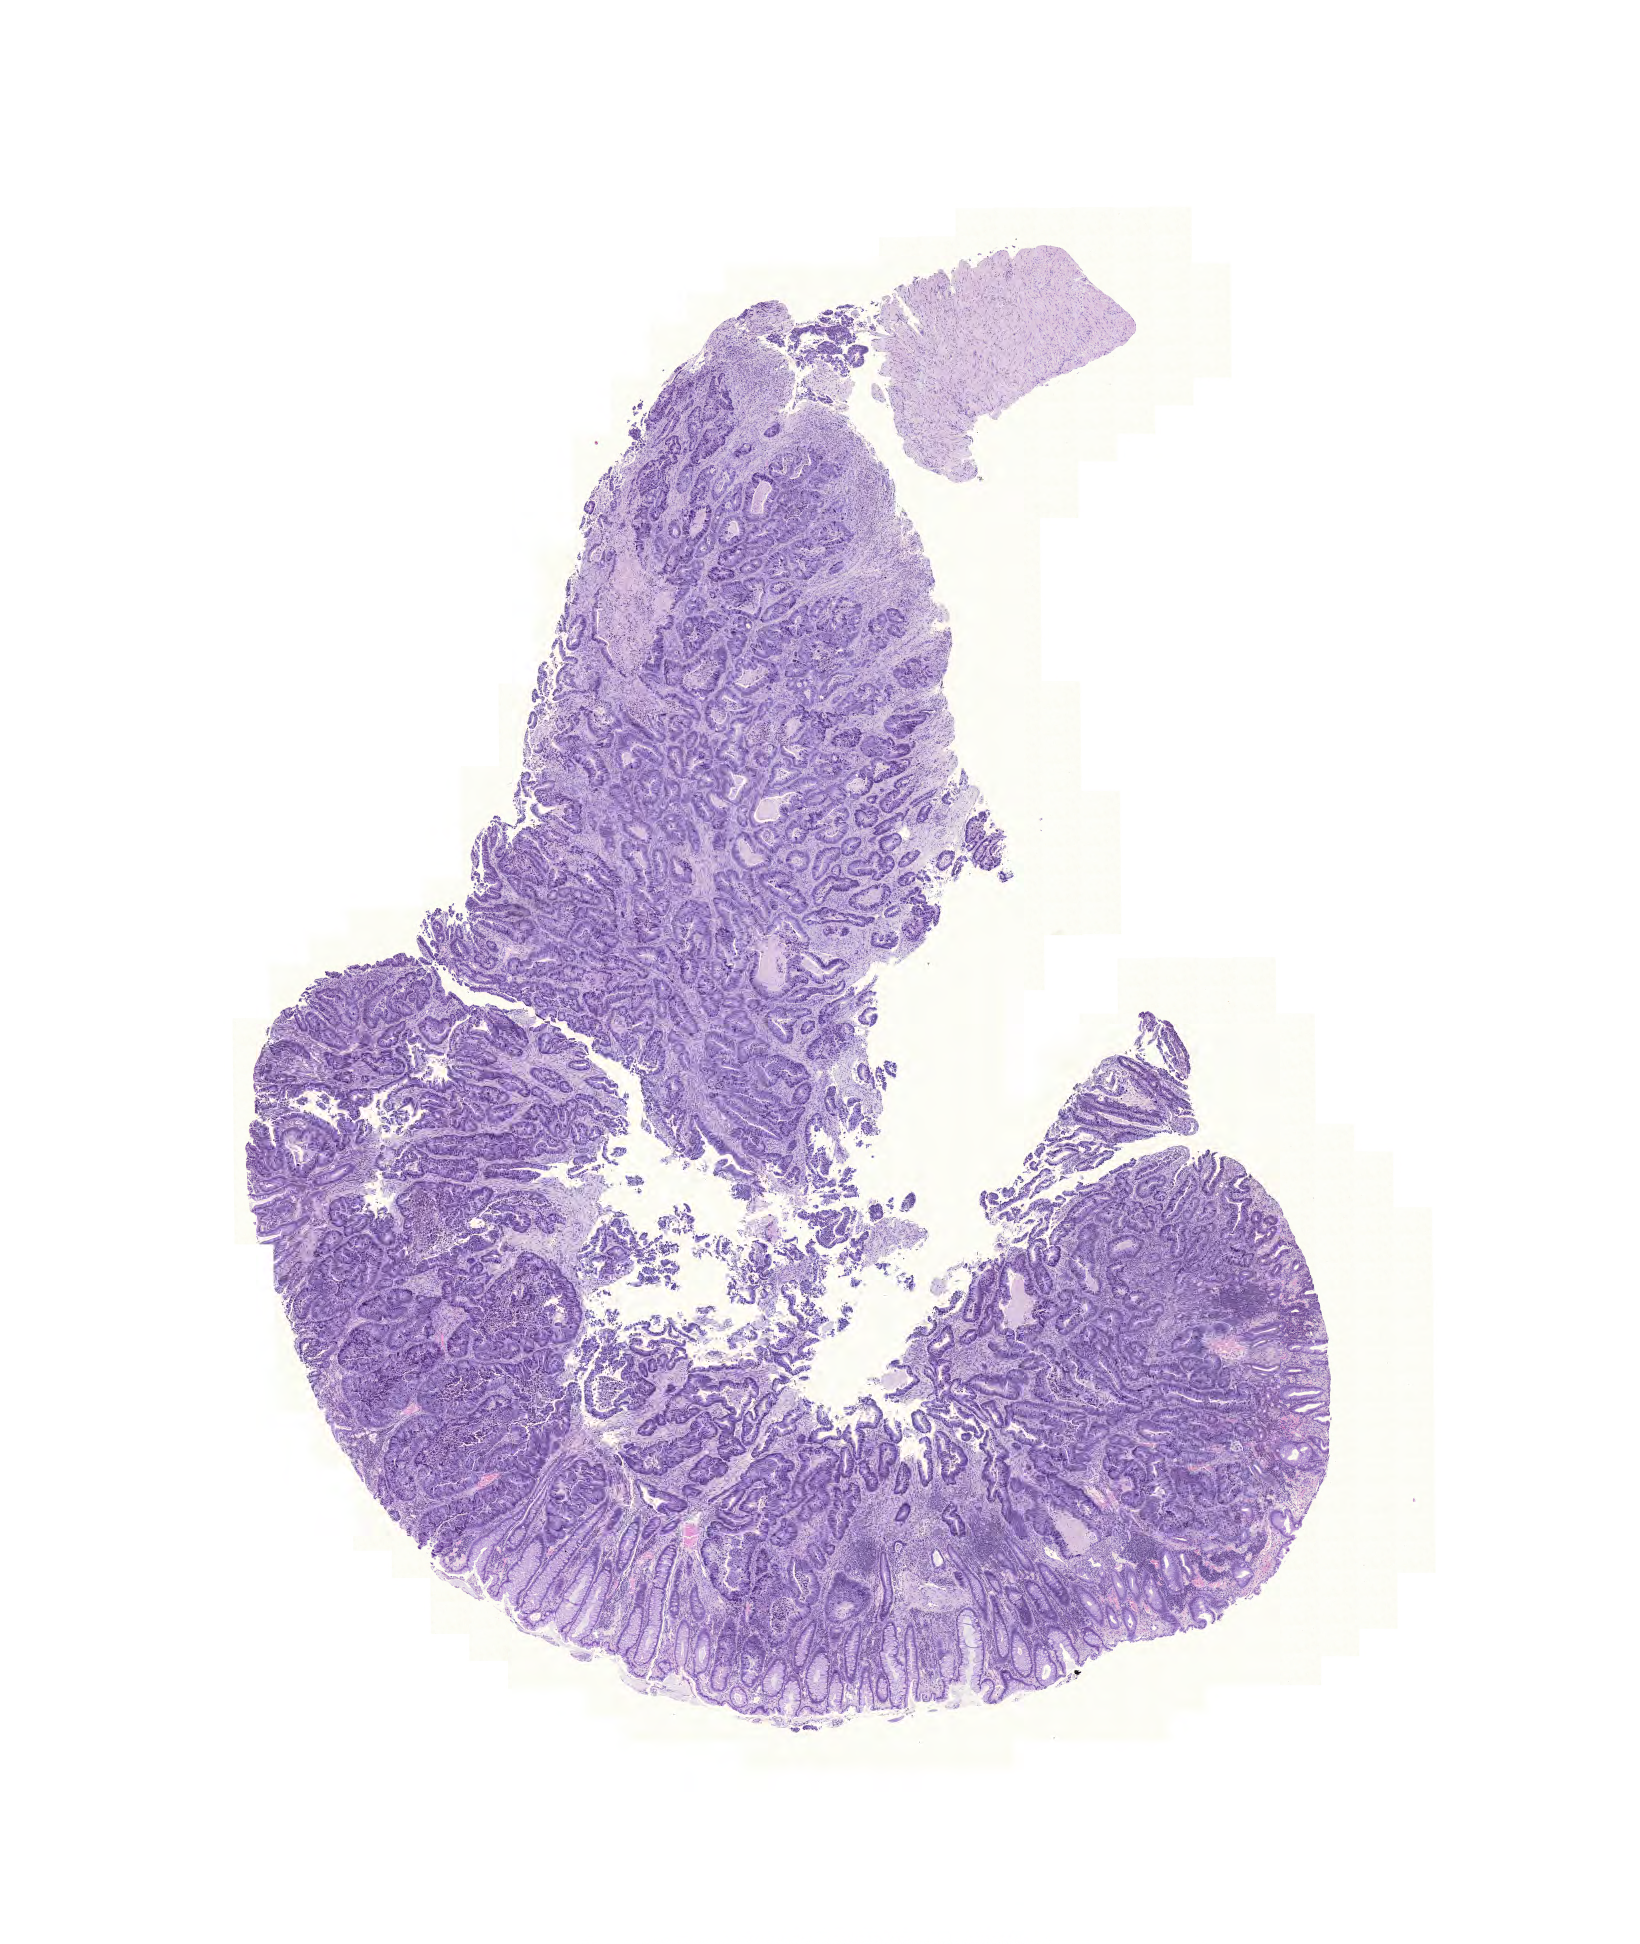
Digitized Hematoxylin and eosin (H&E) stained tissue section (whole slide), whole scanned area (about 12.2 x 14.5 mm, slide scanned at 20x) shown as a low-resolution overview, FFPE section, rectum, primary tumour sample. Male patient; age at initial diagnosis 68 years.
AJCC pathologic stage: IIIB (6th edition). TNM: T4 N1 M0. Diagnosis: Adenocarcinoma, NOS (rectosigmoid junction). Lymph nodes positive (case pathology): 2 of 17 examined.